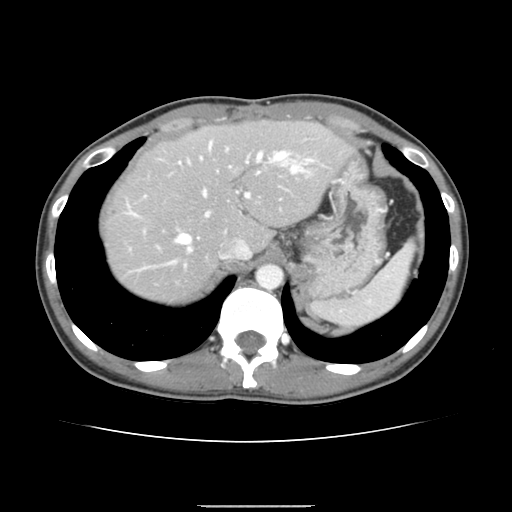
Contrast-enhanced abdominal CT, one axial slice. Slice 114 of 150 in the series (ordered by position). 120 kVp. Intravenous contrast given. Soft-tissue window (W 400 / L 40 HU). 2.5 mm slice thickness. 512 × 512 image matrix, field of view 324 × 324 mm. Female patient, age 32 years. Case-level facts recorded for this patient, not image findings: diagnosis: colorectal cancer liver metastases, imaged before liver resection; multiple liver metastases: yes; largest metastasis: 0.7 cm.
Structures marked on this image (outlined manually by an expert reader):
- hepatic veins: bounding box [x1, y1, x2, y2] px = [131, 150, 297, 271]
- liver: [104, 122, 348, 302]
- planned liver remnant (the part of the liver to remain after resection): [103, 121, 349, 265]
- portal vein (with intrahepatic branches): [179, 142, 314, 216]